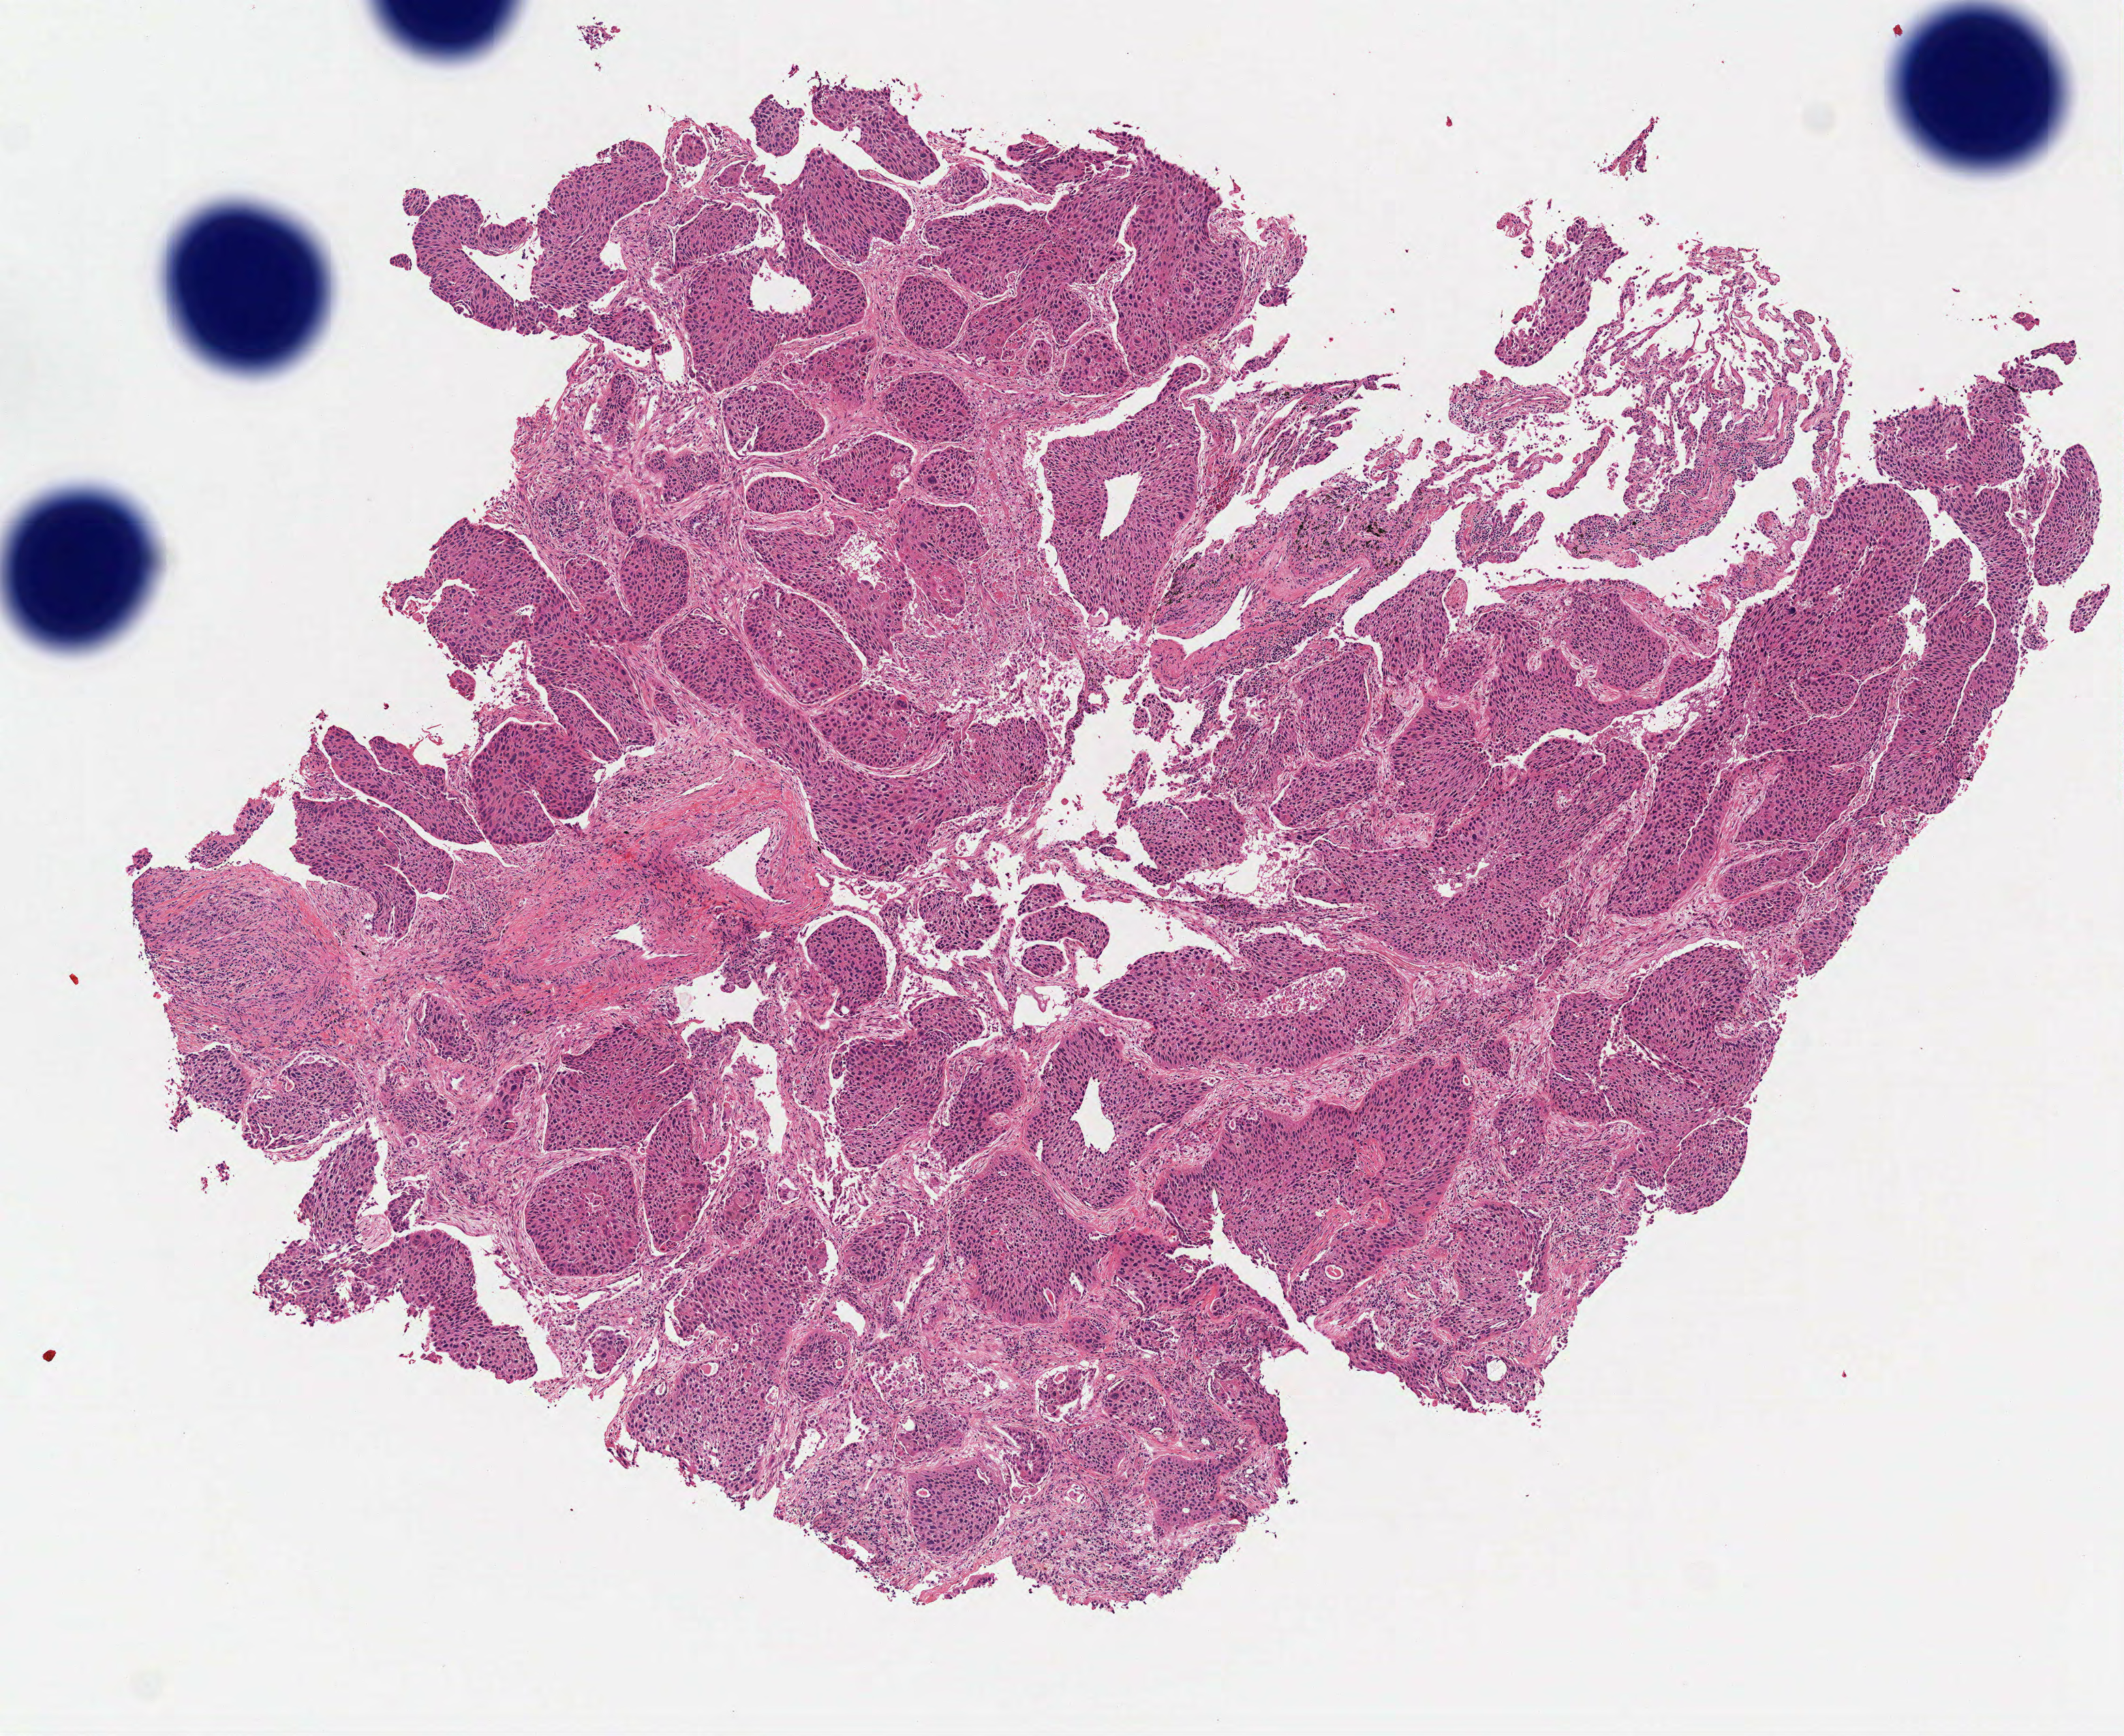
Whole-slide histology image, H&E-stained, a low-resolution overview of the entire scanned area, about 6.3 x 5.1 mm (slide scanned at 40x), frozen section from the top of the tissue portion, sample: primary tumour, lung. Male patient; age at initial diagnosis 75 years. Slide review estimates, as recorded: tumour cells 90%, tumour nuclei 75%, normal cells 0%, stromal cells 10%, necrosis 0%. Inflammatory infiltration, as recorded: lymphocyte infiltration 10%, monocyte infiltration 0%, neutrophil infiltration 5%.
• diagnosis: Squamous cell carcinoma, NOS (upper lobe, lung)
• TNM: T2 N0 M0
• AJCC pathologic stage: IB